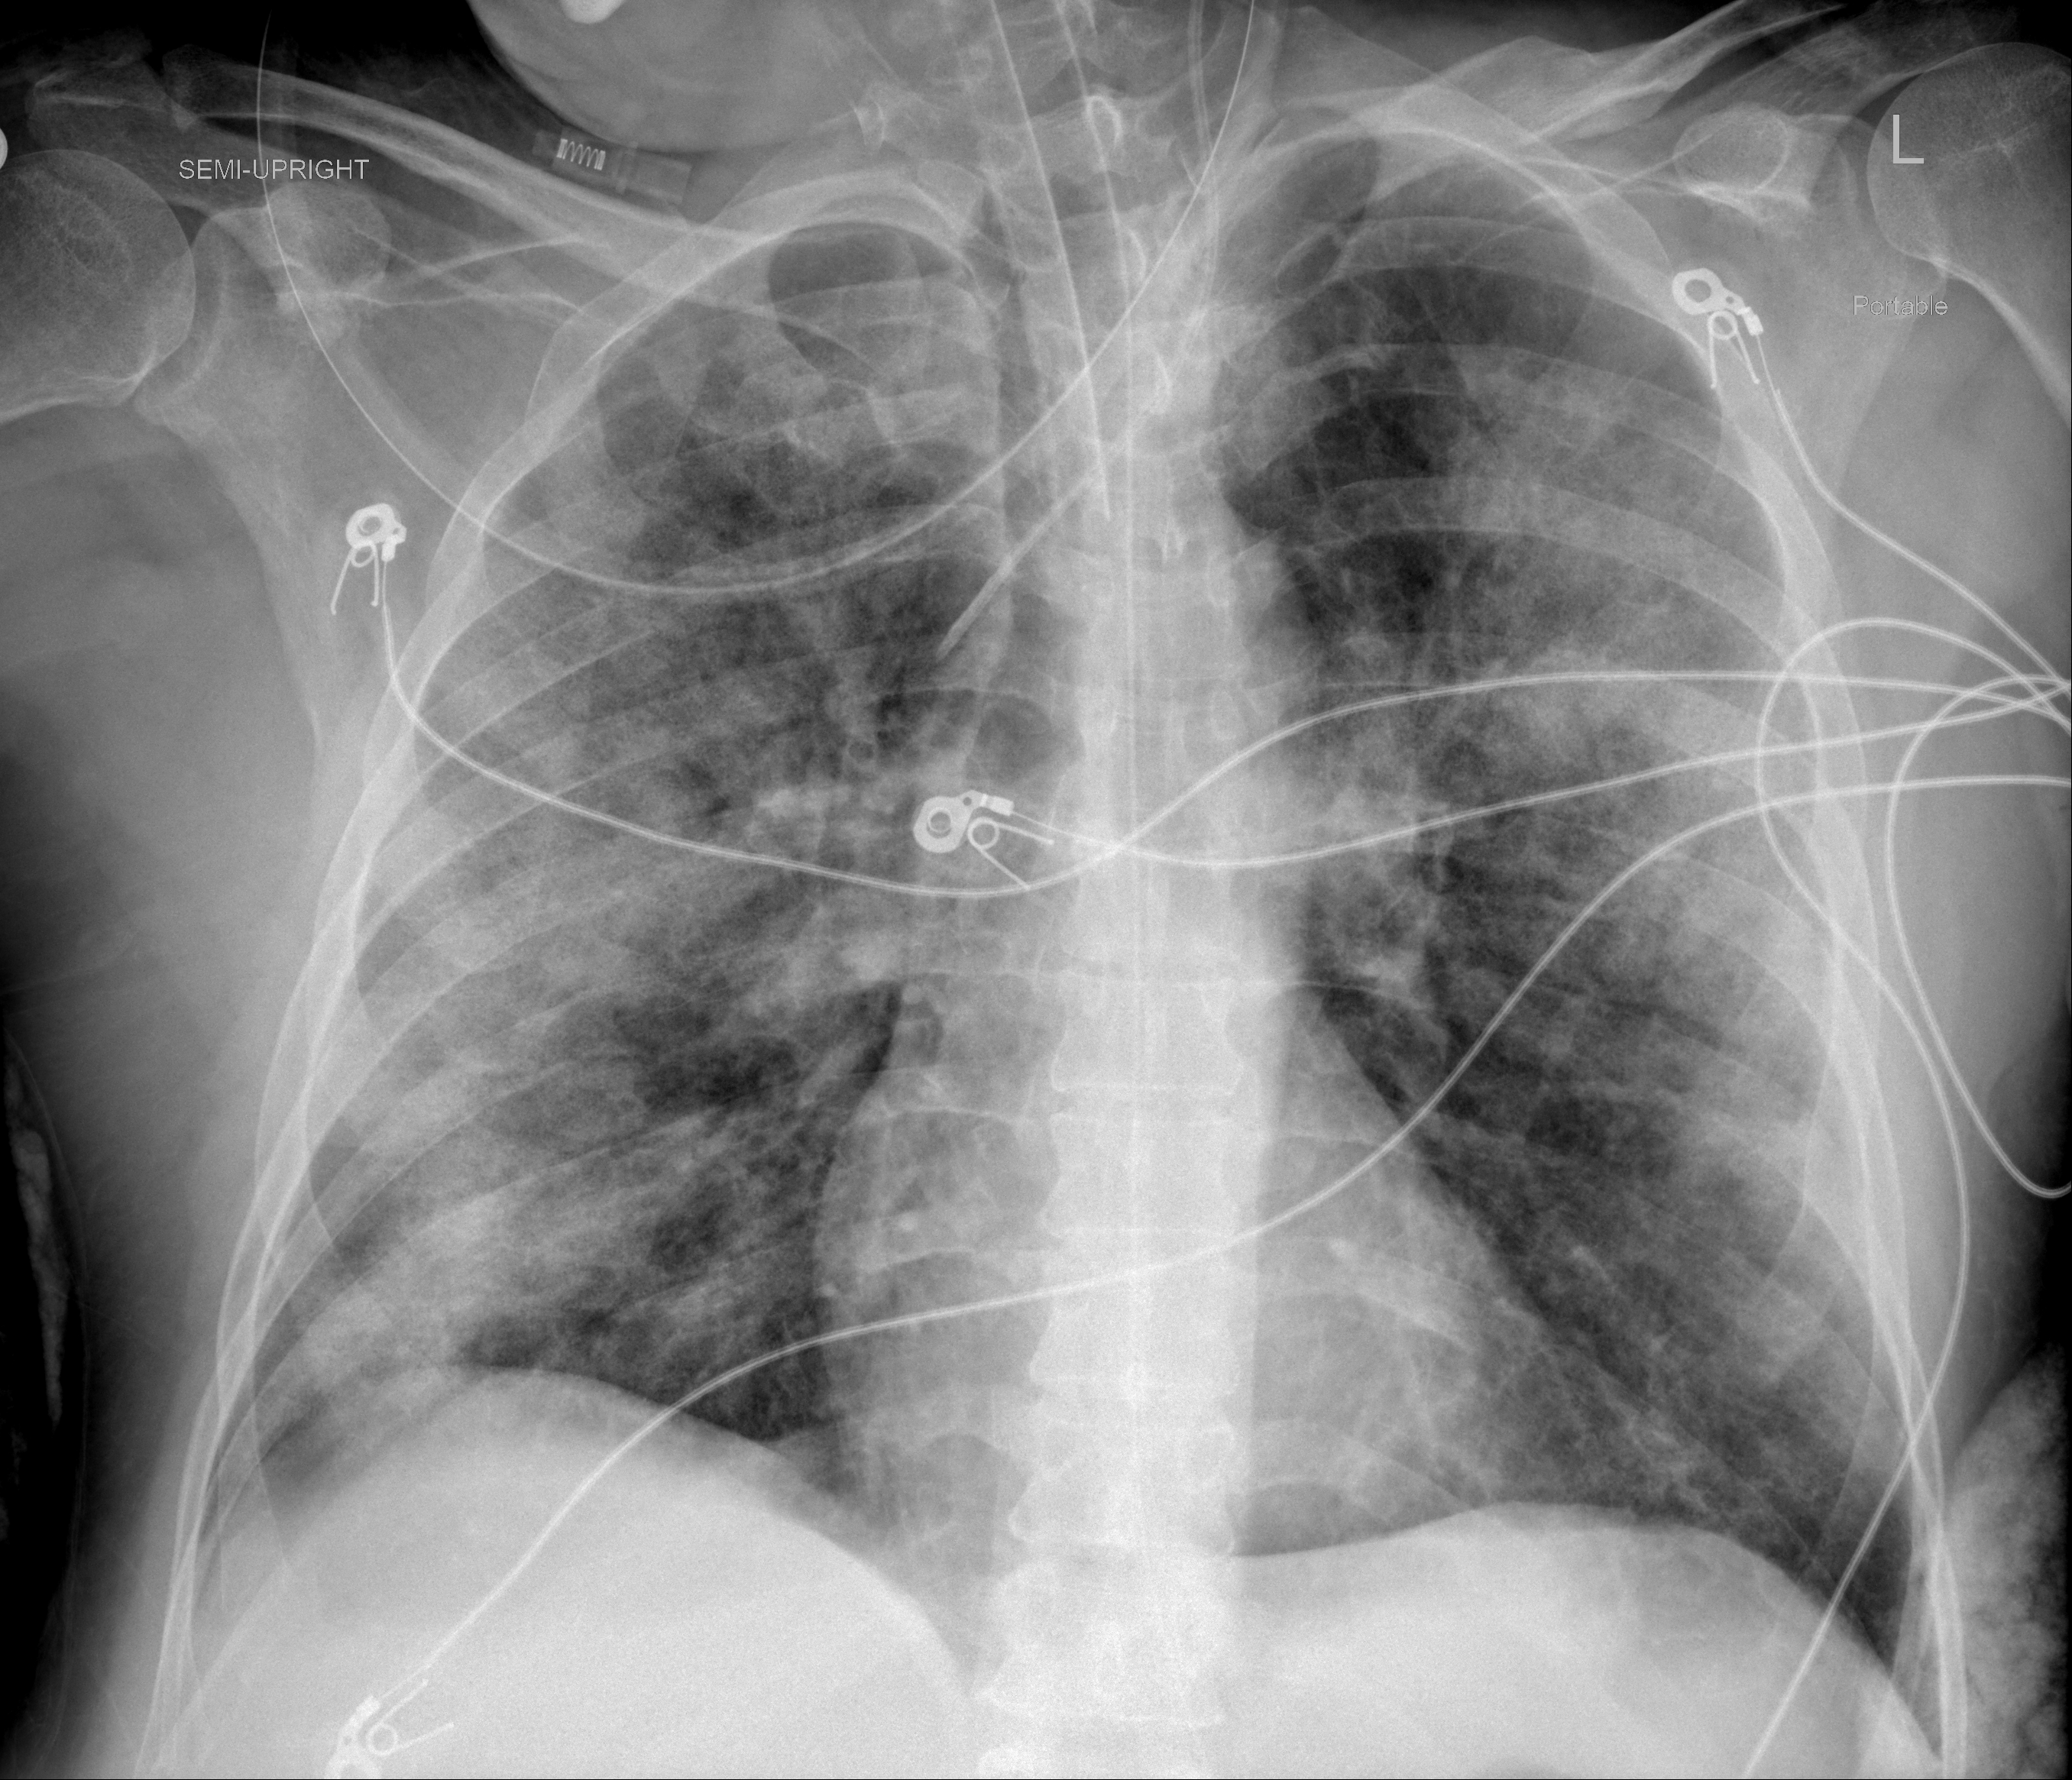
Portable chest radiograph, AP projection. Male patient, age 57 years; imaged 6 days after the COVID-19 diagnosis.
Radiologist key findings (as recorded): There is been interval improvement in somewhat confluent diffuse airspace opacities throughout both lungs.